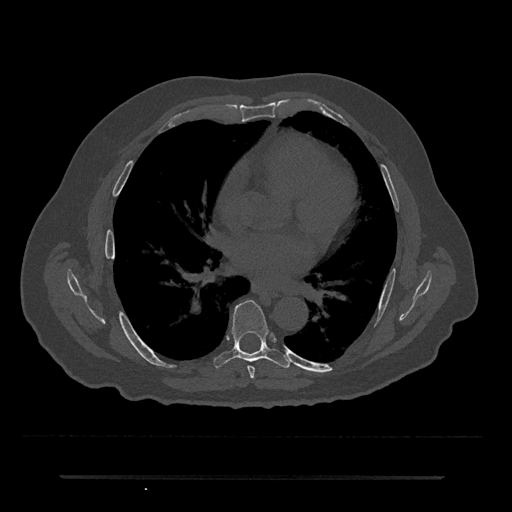
CT including the spine, one axial slice; position 394 of 797 along the scan axis; 120 kVp; bone window (W 1800 / L 400 HU); 0.5 mm slice thickness; 512 × 512 image matrix, field of view 437 × 437 mm. Patient: male, 69 years. Case-level facts recorded for this patient, not image findings: primary cancer: prostate.
Annotated regions visible in this slice (semi-automatically segmented with operator editing):
- T6 vertebra: box from (x=248, y=366) to (x=255, y=379) px
- T7 vertebra: (x=214, y=300)–(x=290, y=368)